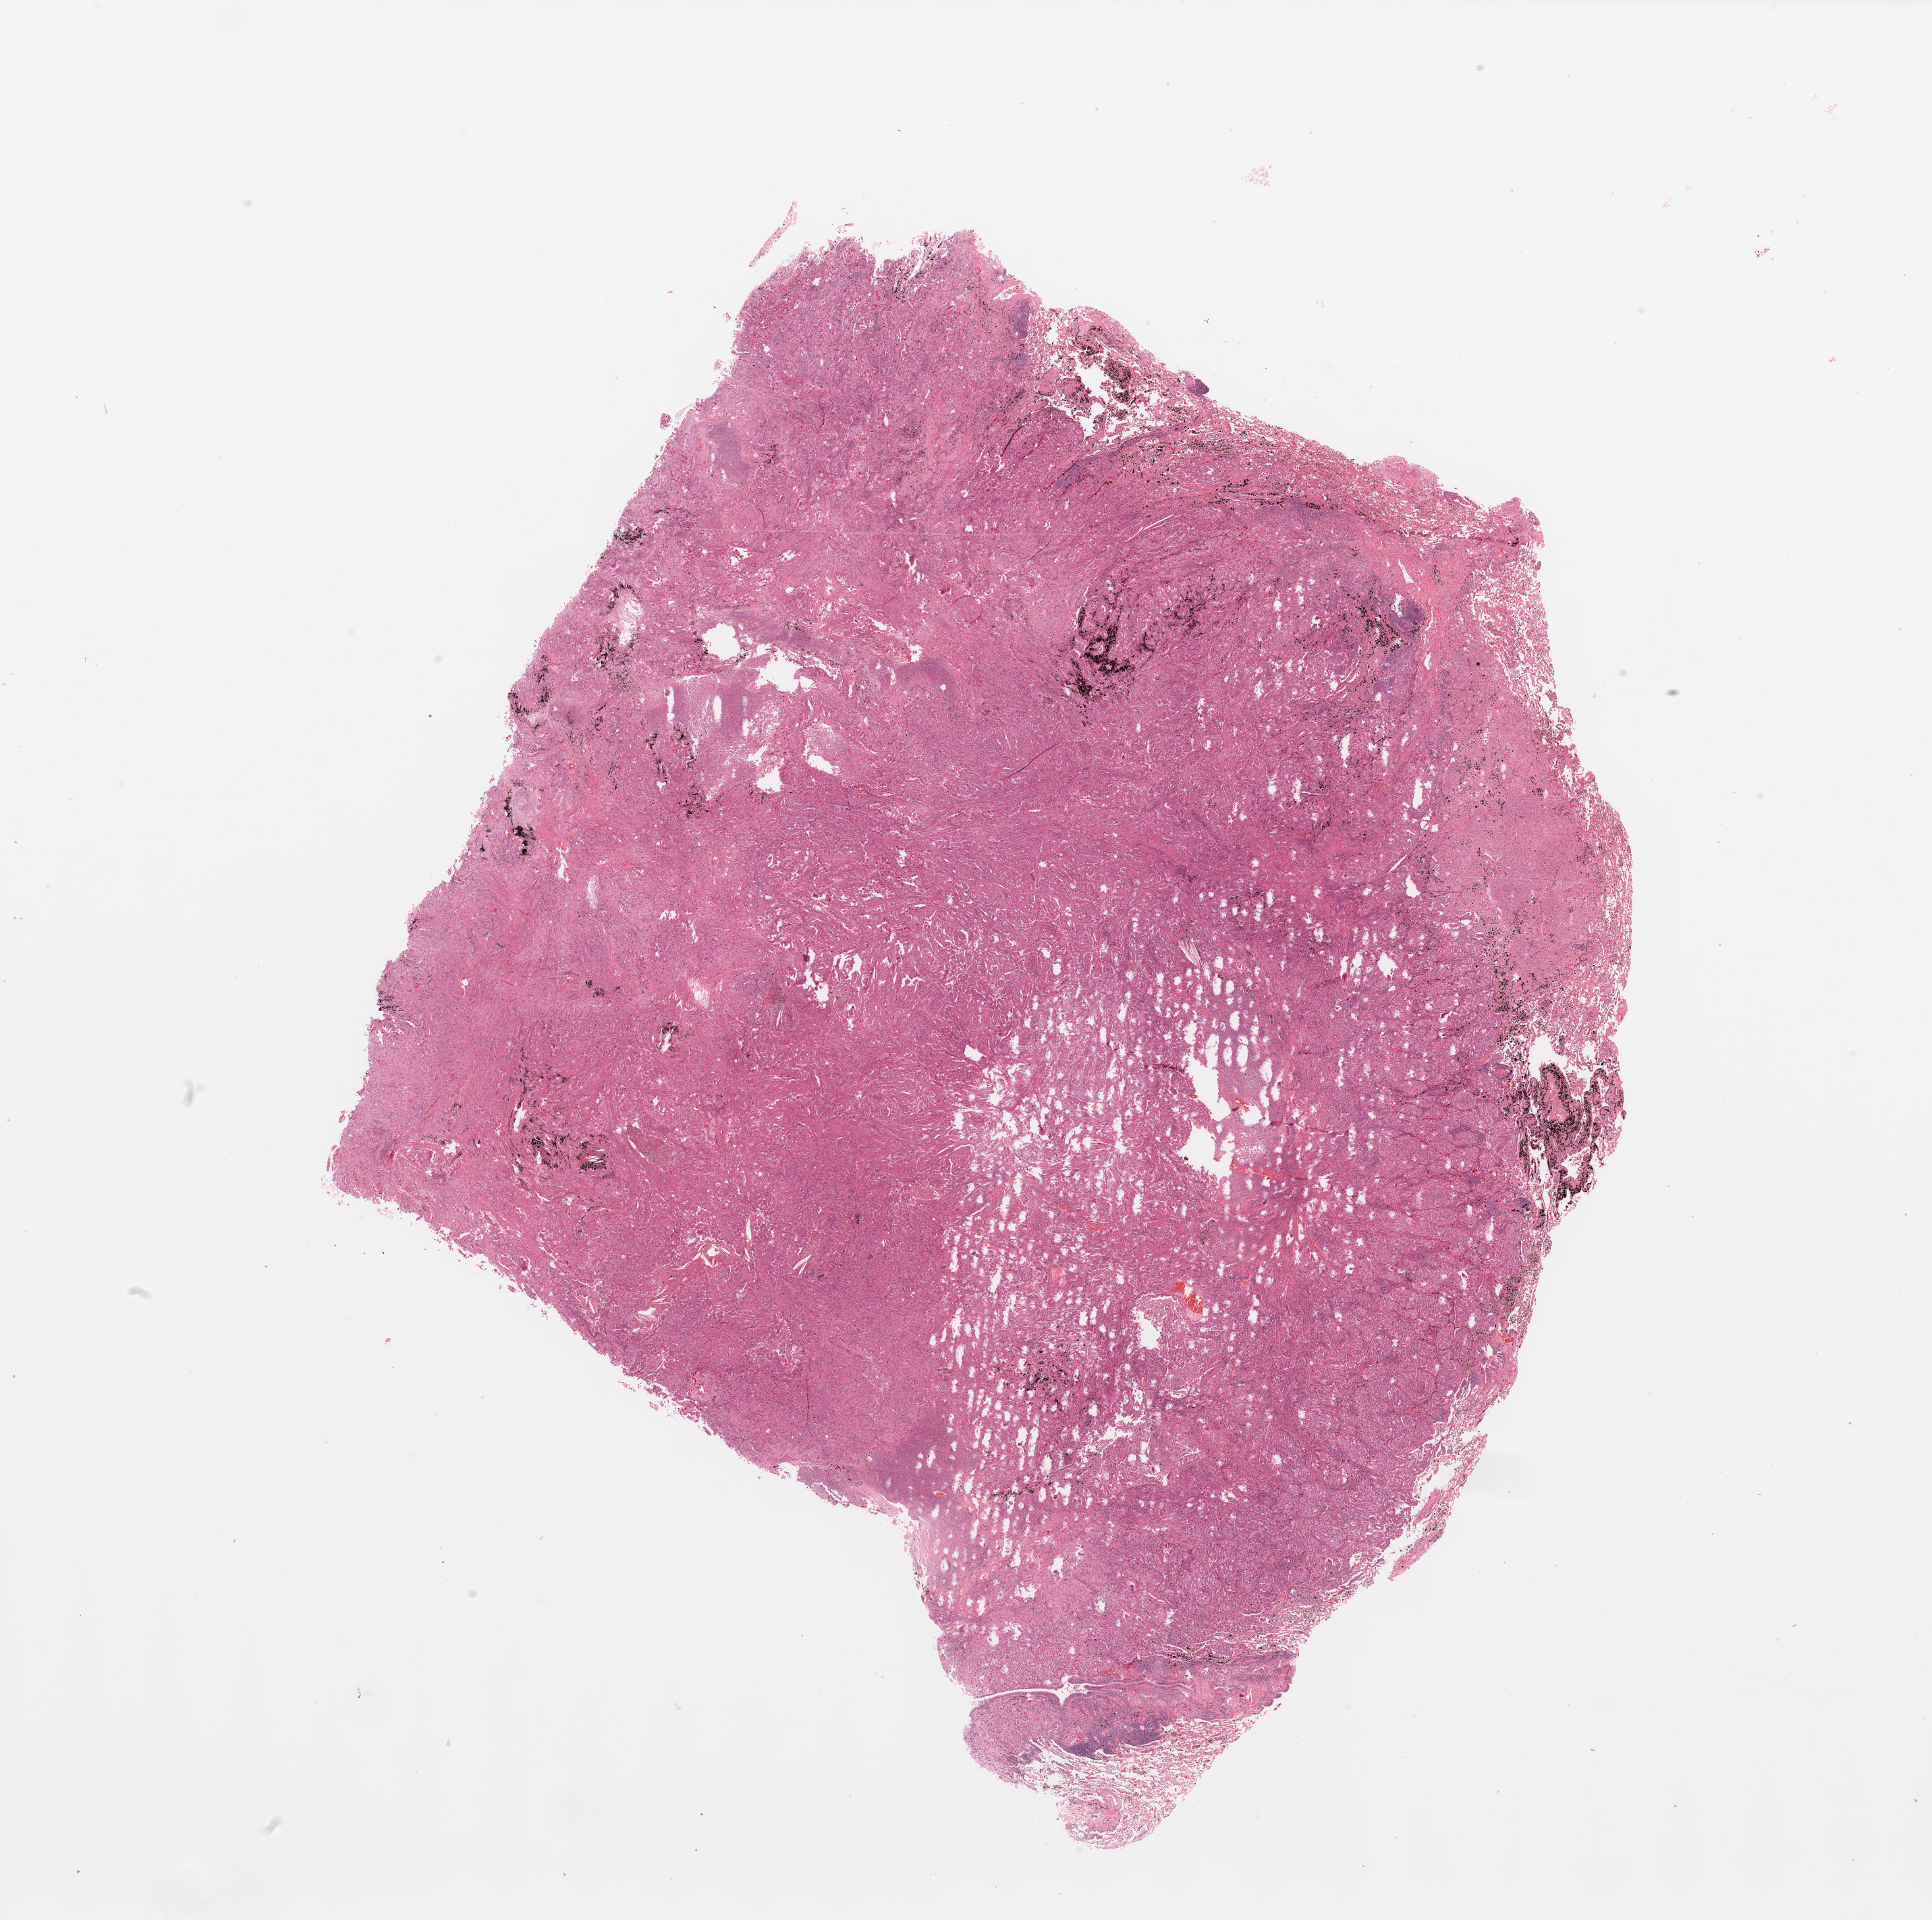
Digitized H&E tissue section (whole slide) — shown as a low-resolution overview of the whole scanned area (about 22.6 x 22.5 mm, slide scanned at 20x). Tumour tissue sample, sampled site: lung. 71-year-old male patient. Histologic grade: G3 (poorly differentiated). Pathologist review of this section (percent, as recorded): tumour nuclei 75%, necrosis 5%.
* AJCC pathologic stage: IIIA
* histologic diagnosis: Adenocarcinoma, NOS